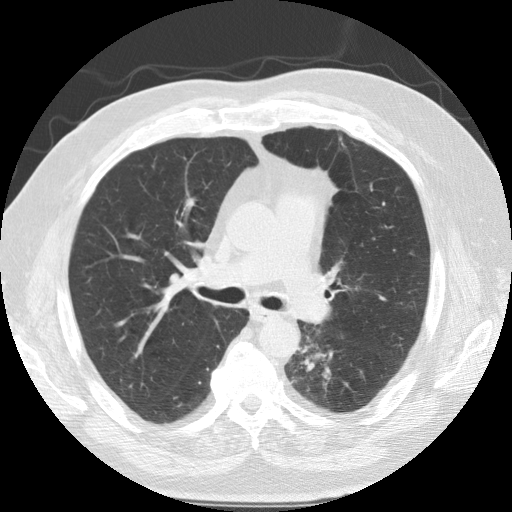
Low-dose screening chest CT, one axial slice. Slice 74 of 124 in the series (ordered by position). 120 kVp. Lung window (W 1500 / L -600 HU). 512 × 512 image matrix, field of view 360 × 360 mm.
Structures marked on this image (outlined manually by an expert reader):
- lesion 1 (tumor, lower lobe of left lung): bounding box (x1, y1, x2, y2) in pixels: (301, 353, 331, 381)